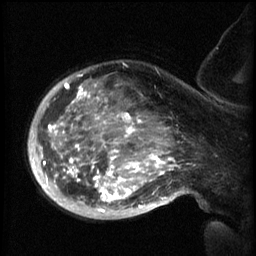
Breast MRI (dynamic contrast-enhanced), one sagittal slice; slice 45 of 60 in the series (ordered by position); 3 images stored at this slice position (order not interpretable as contrast timing); 1.5 T; TE 4.2 ms, TR 8.2 ms; 2.3 mm slice thickness; 256 × 256 image matrix. Female patient, age 50 years.
Outlined on this slice (semi-automatic segmentation, software-assisted and operator-edited):
- analysis volume of interest (the breast-tissue region the enhancement analysis was run in; not a lesion): box from (x=50, y=66) to (x=169, y=217) px
- tumour enhancement mask (voxels above the 70 % enhancement threshold inside the analysis volume of interest): (x=50, y=74)–(x=169, y=213)